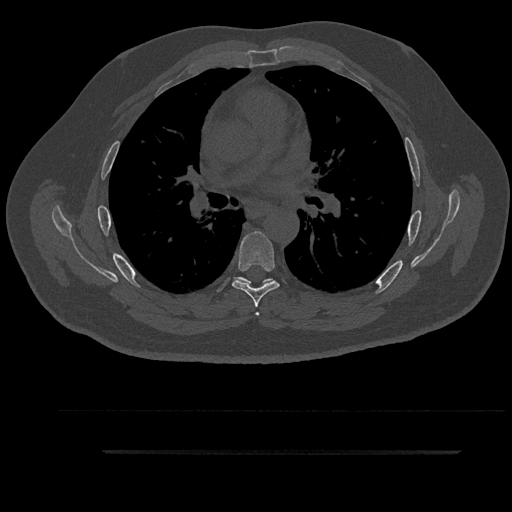
CT including the spine, one axial slice; position 574 of 797 along the scan axis; reconstruction kernel Br40s/3; 120 kVp; bone window (W 1800 / L 400 HU); 0.5 mm slice thickness; 512 × 512 image matrix, field of view 432 × 432 mm. Male patient, age 63 years. From the clinical record (not read from this slice): primary cancer: renal.
Structures marked on this image (semi-automatically segmented with operator editing):
- T5 vertebra: bounding box [x1, y1, x2, y2] px = [235, 277, 273, 316]
- T6 vertebra: [232, 231, 280, 307]
- T7 vertebra: [242, 279, 275, 284]